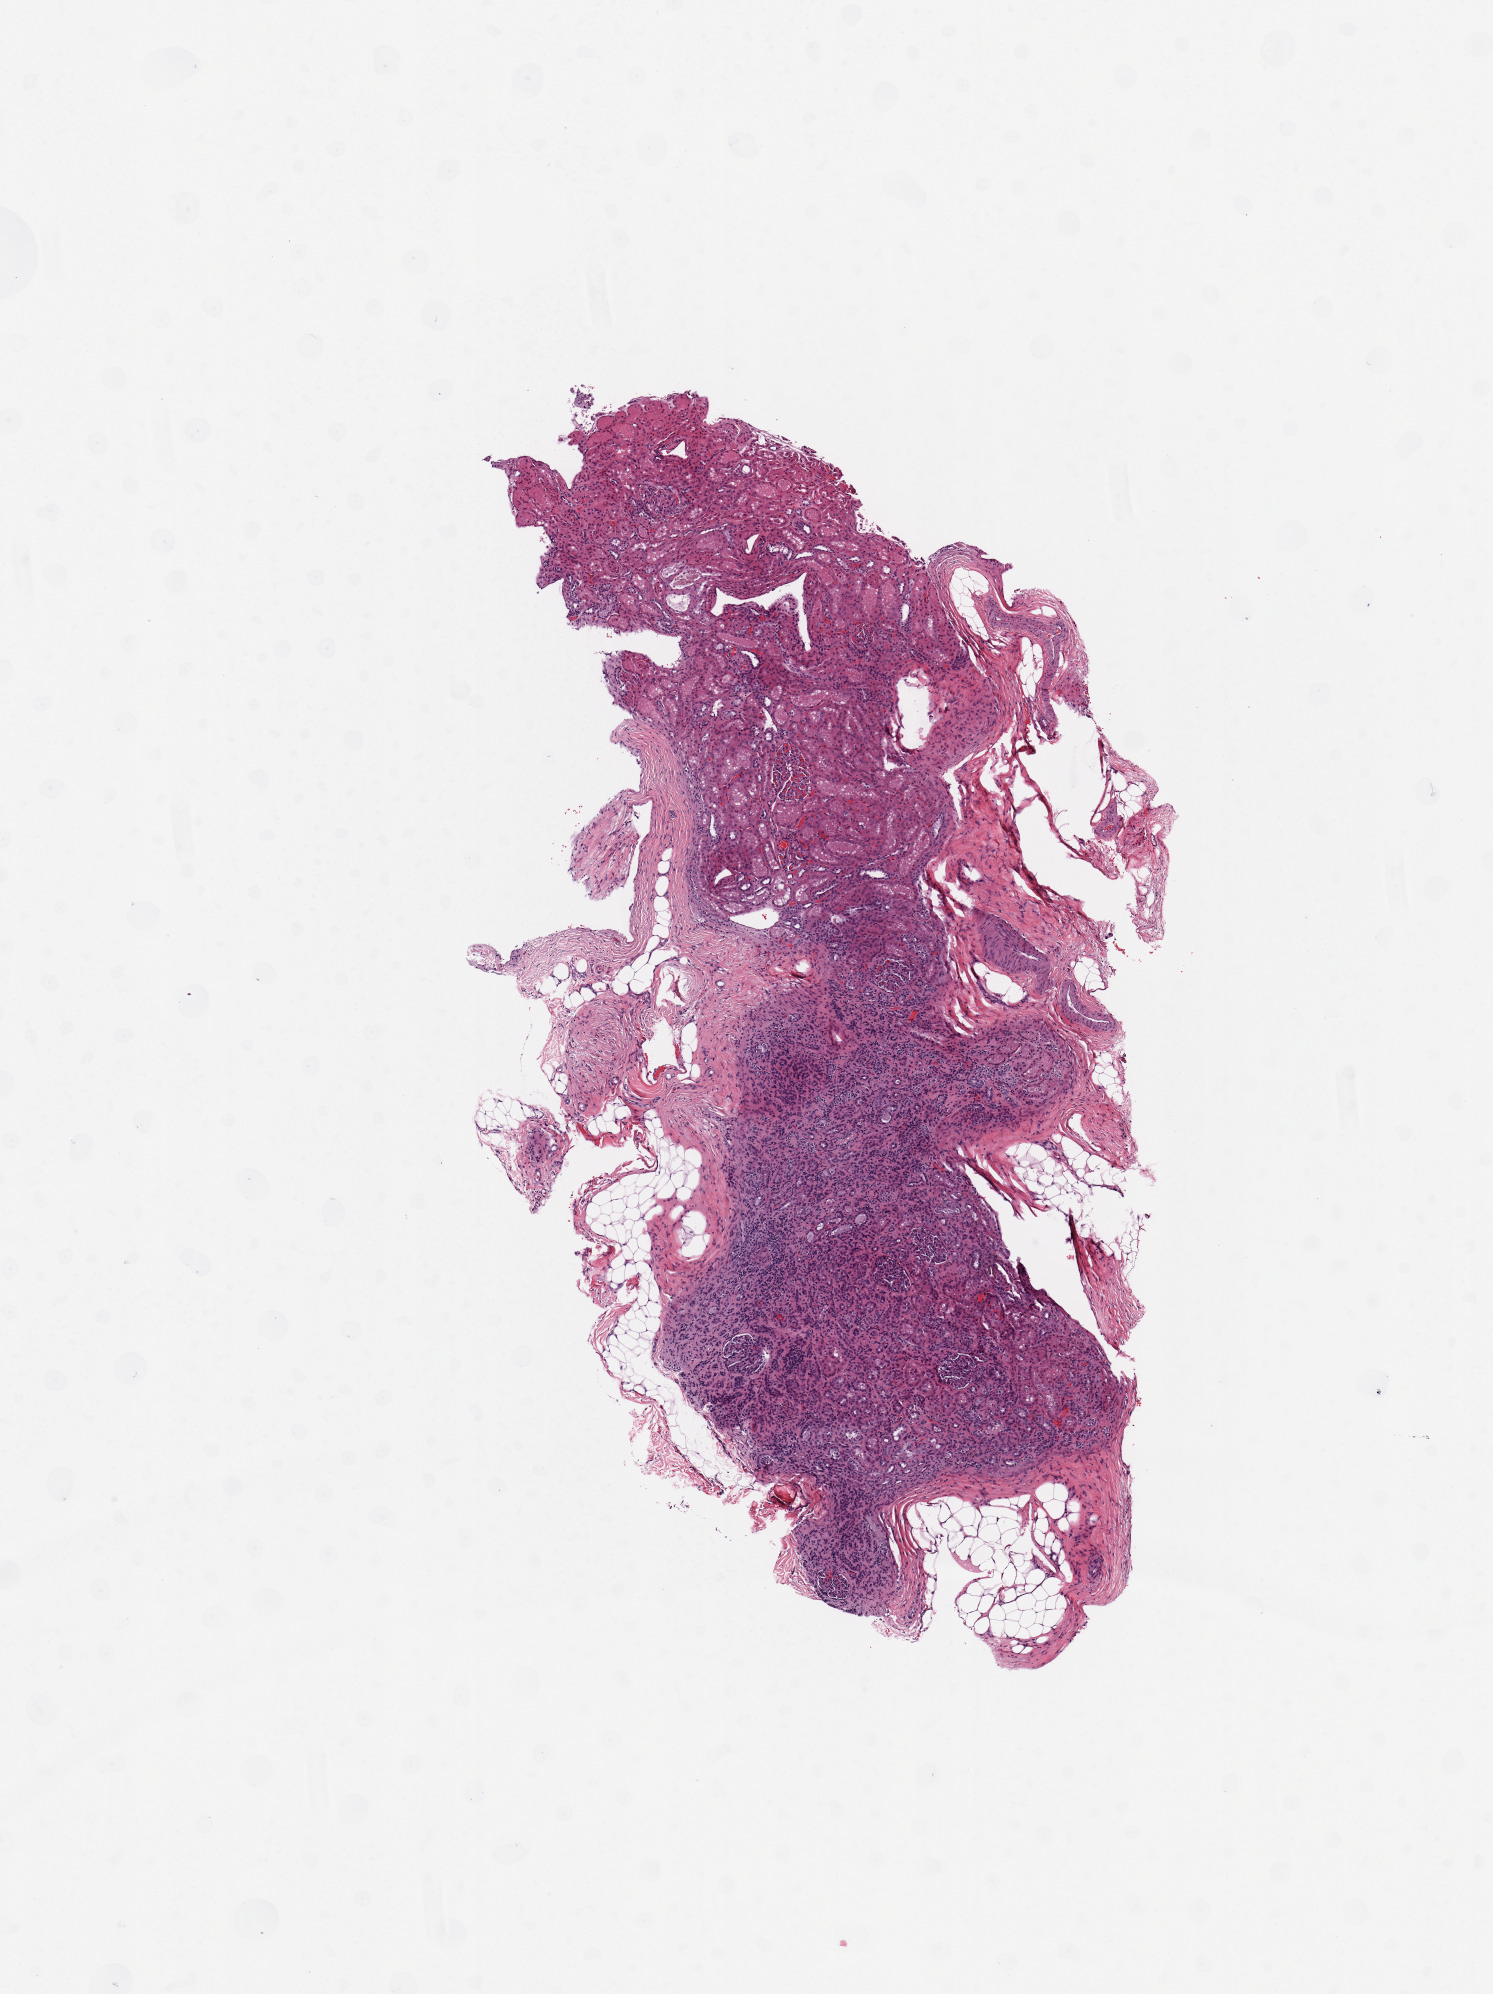
Whole-slide histology image, H&E — whole scanned area (about 5.9 x 7.9 mm, slide scanned at 20x) shown as a low-resolution overview, kidney, normal (non-tumour) tissue. 33-year-old female patient.
This section: normal (non-tumour) tissue from the same patient. Patient diagnosis: Renal cell carcinoma, NOS.